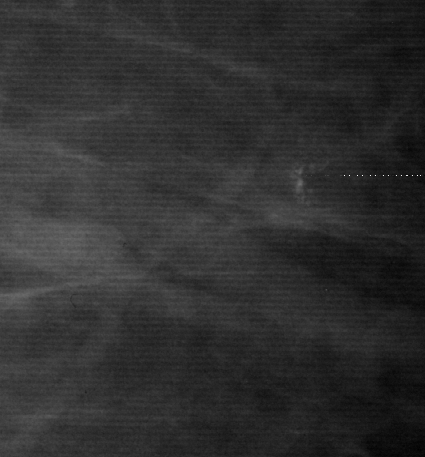
Region of interest cut from a scanned film mammogram (one marked finding), right breast, CC view.
Marked abnormality: calcifications, morphology amorphous, distribution clustered; BI-RADS assessment category 4; pathology (as recorded): benign.